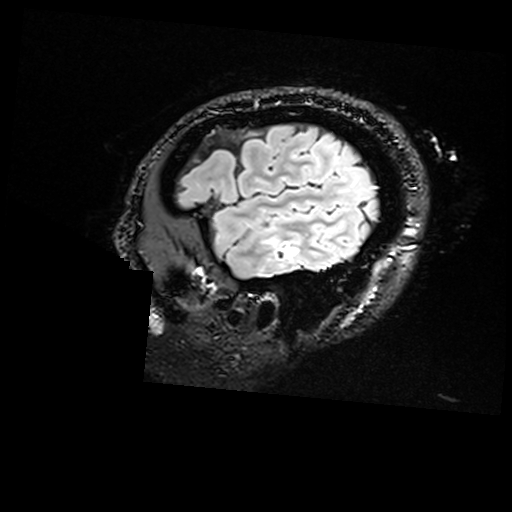
Brain MRI from a brain-tumour surgery series, one sagittal slice; T2 FLAIR; 1 mm slice thickness; 512 × 512 image matrix, field of view 250 × 250 mm. From the clinical record (not read from this slice): histopathology: Non-tumor destructive chronic inflammatory lesion with abnormal vasculature; tumour location: Right Inferior Temporal.
Outlined on this slice (outlined manually by an expert reader):
- residual tumour: bounding box (x1, y1, x2, y2) in pixels: (285, 245, 293, 259)